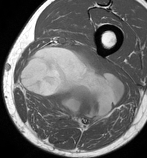
MRI of an extremity soft-tissue mass, one axial slice; slice 44 of 86 in the series (ordered by position); MR volume resampled by the dataset authors to the PET/CT grid (not the native acquisition matrix); 3.27 mm slice thickness; 147 × 158 image matrix, field of view 144 × 154 mm. Male patient. From the clinical record (not read from this slice): histological type: undifferentiated pleomorphic liposarcoma; grade: high; site of the primary tumour: left thigh.
Annotated regions visible in this slice (expert contour drawn on MRI and transferred to this co-registered scan by the dataset authors):
- gross tumour volume including surrounding oedema: bounding box (x1, y1, x2, y2) in pixels: (19, 46, 125, 130)
- gross tumour volume (mass): (21, 46, 125, 130)